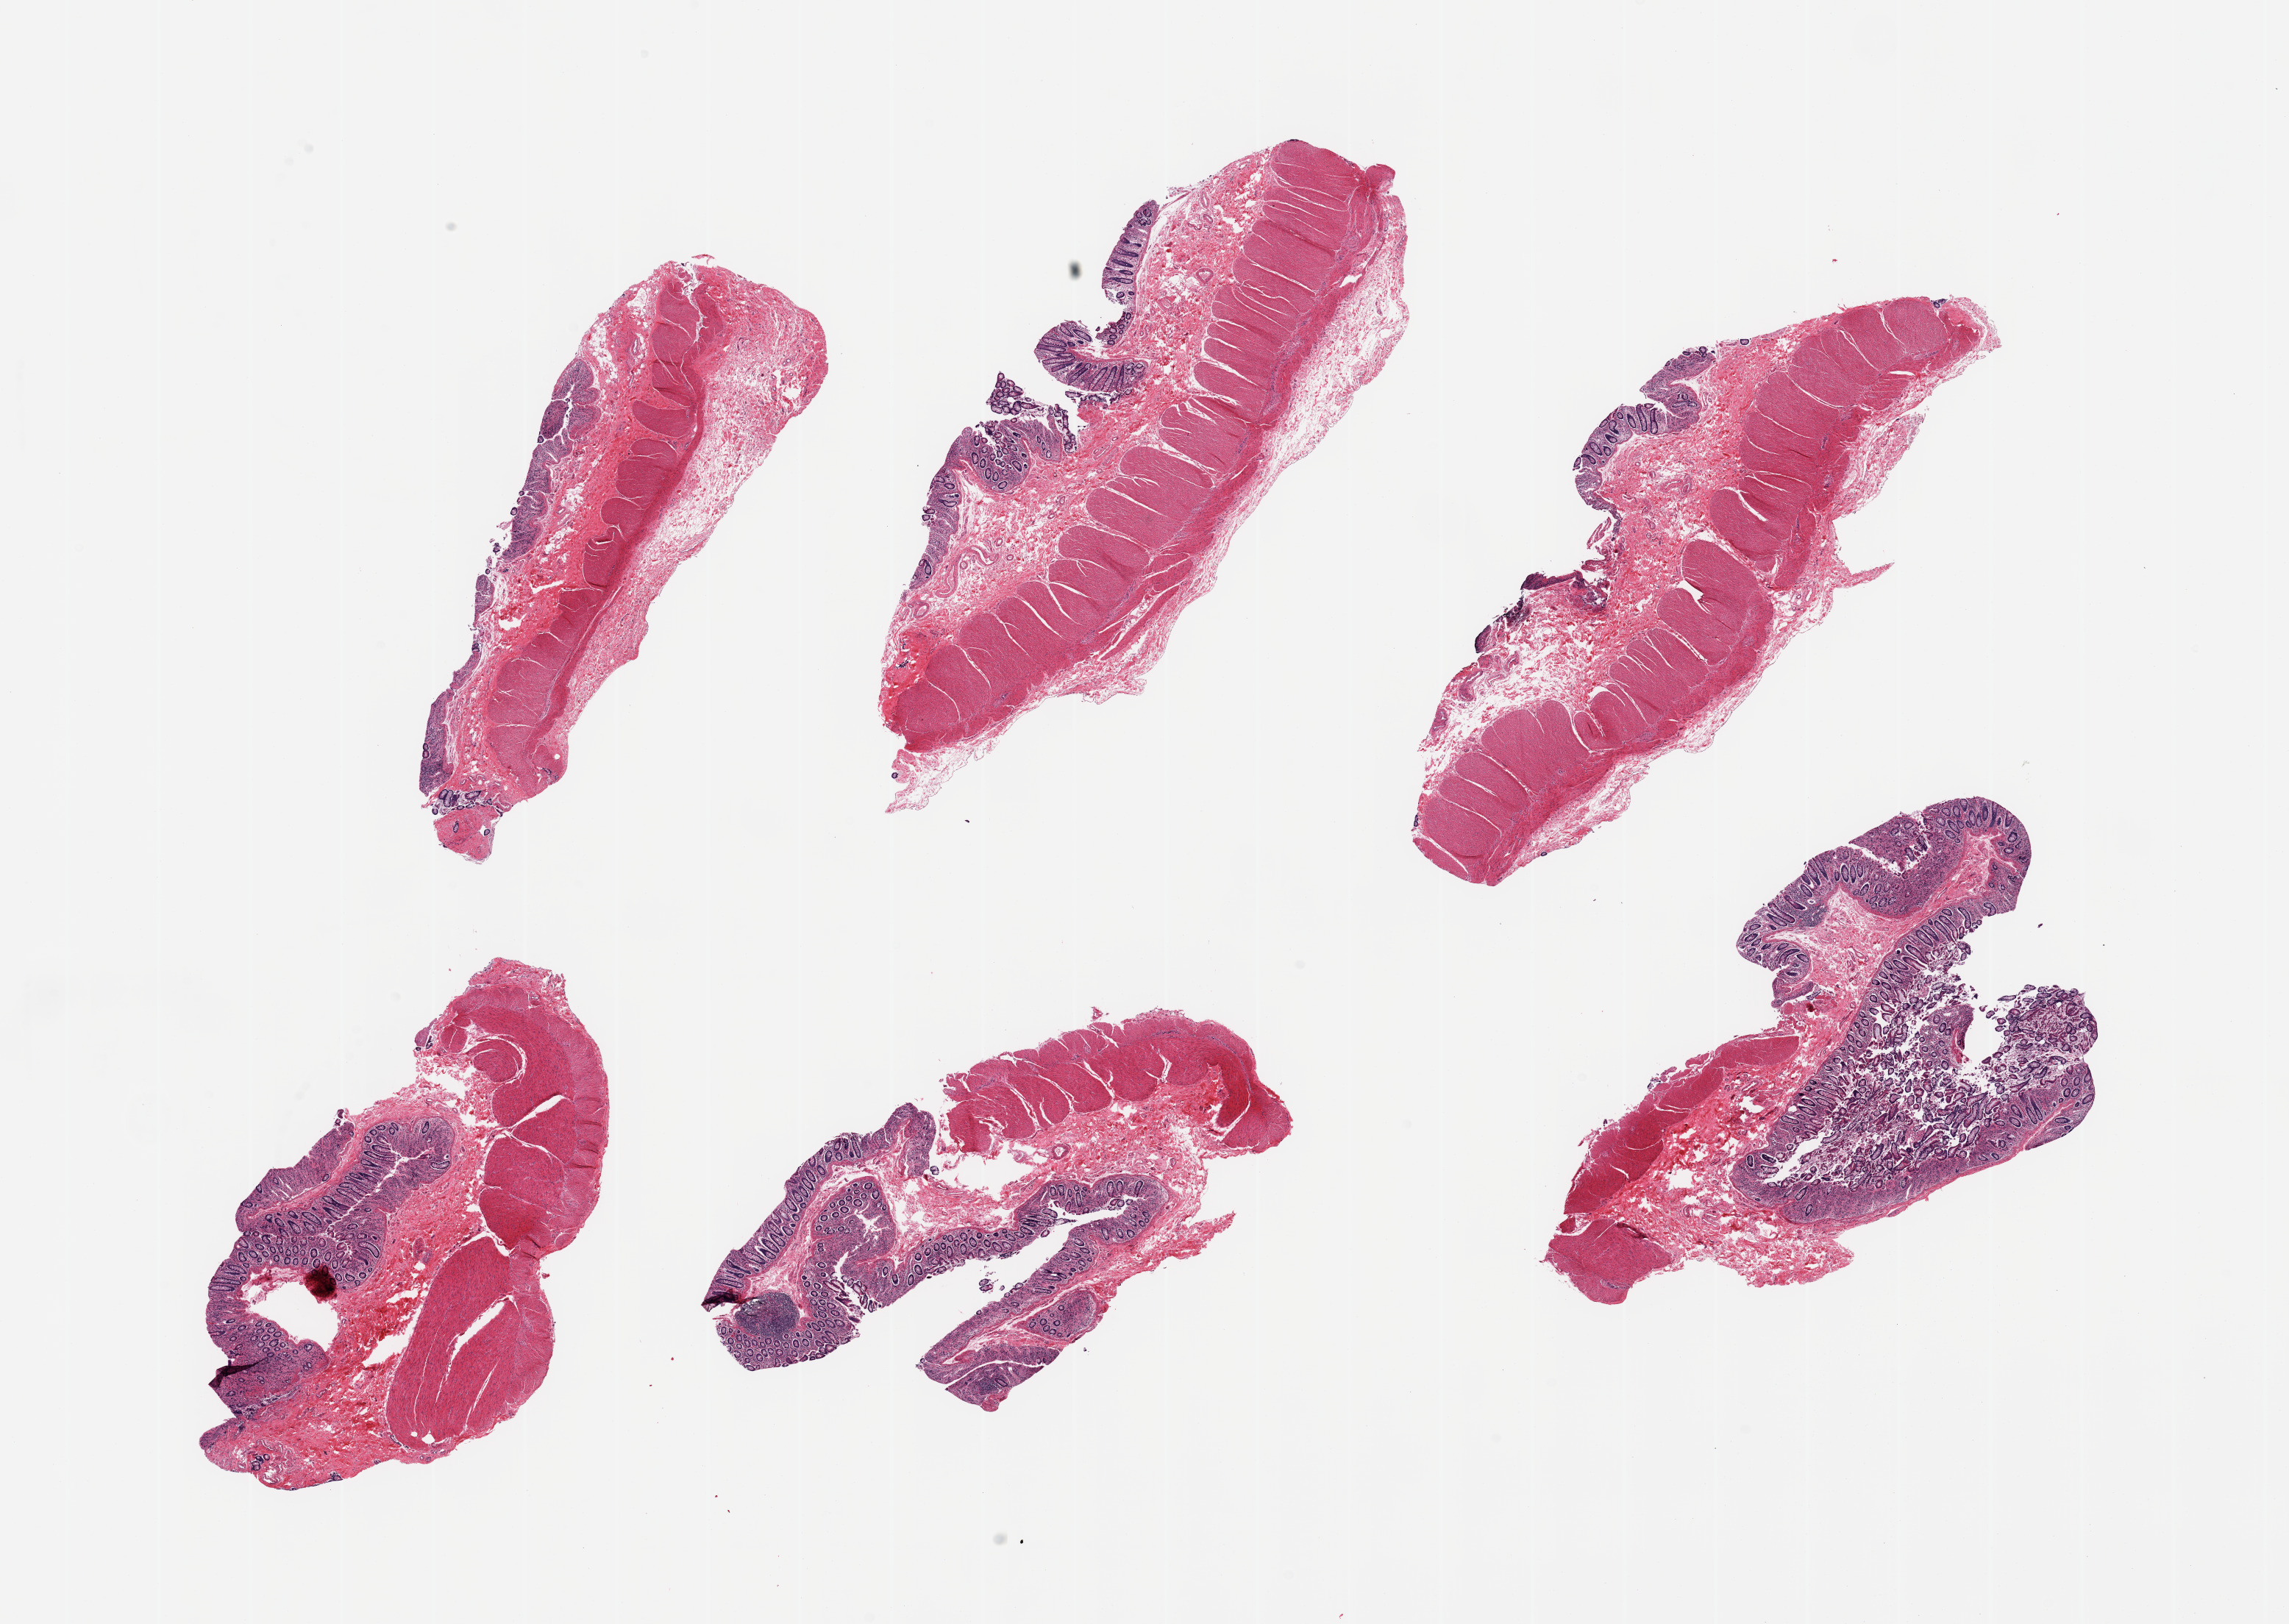
Whole-slide image, H&E stain, a low-resolution overview of the entire scanned area, about 24.6 x 17.5 mm (acquisition: 20x scan); PAXgene-fixed paraffin-embedded (PFPE) section; target tissue: transverse colon; tissue donor sample.
Review note (as recorded): 6 pieces.